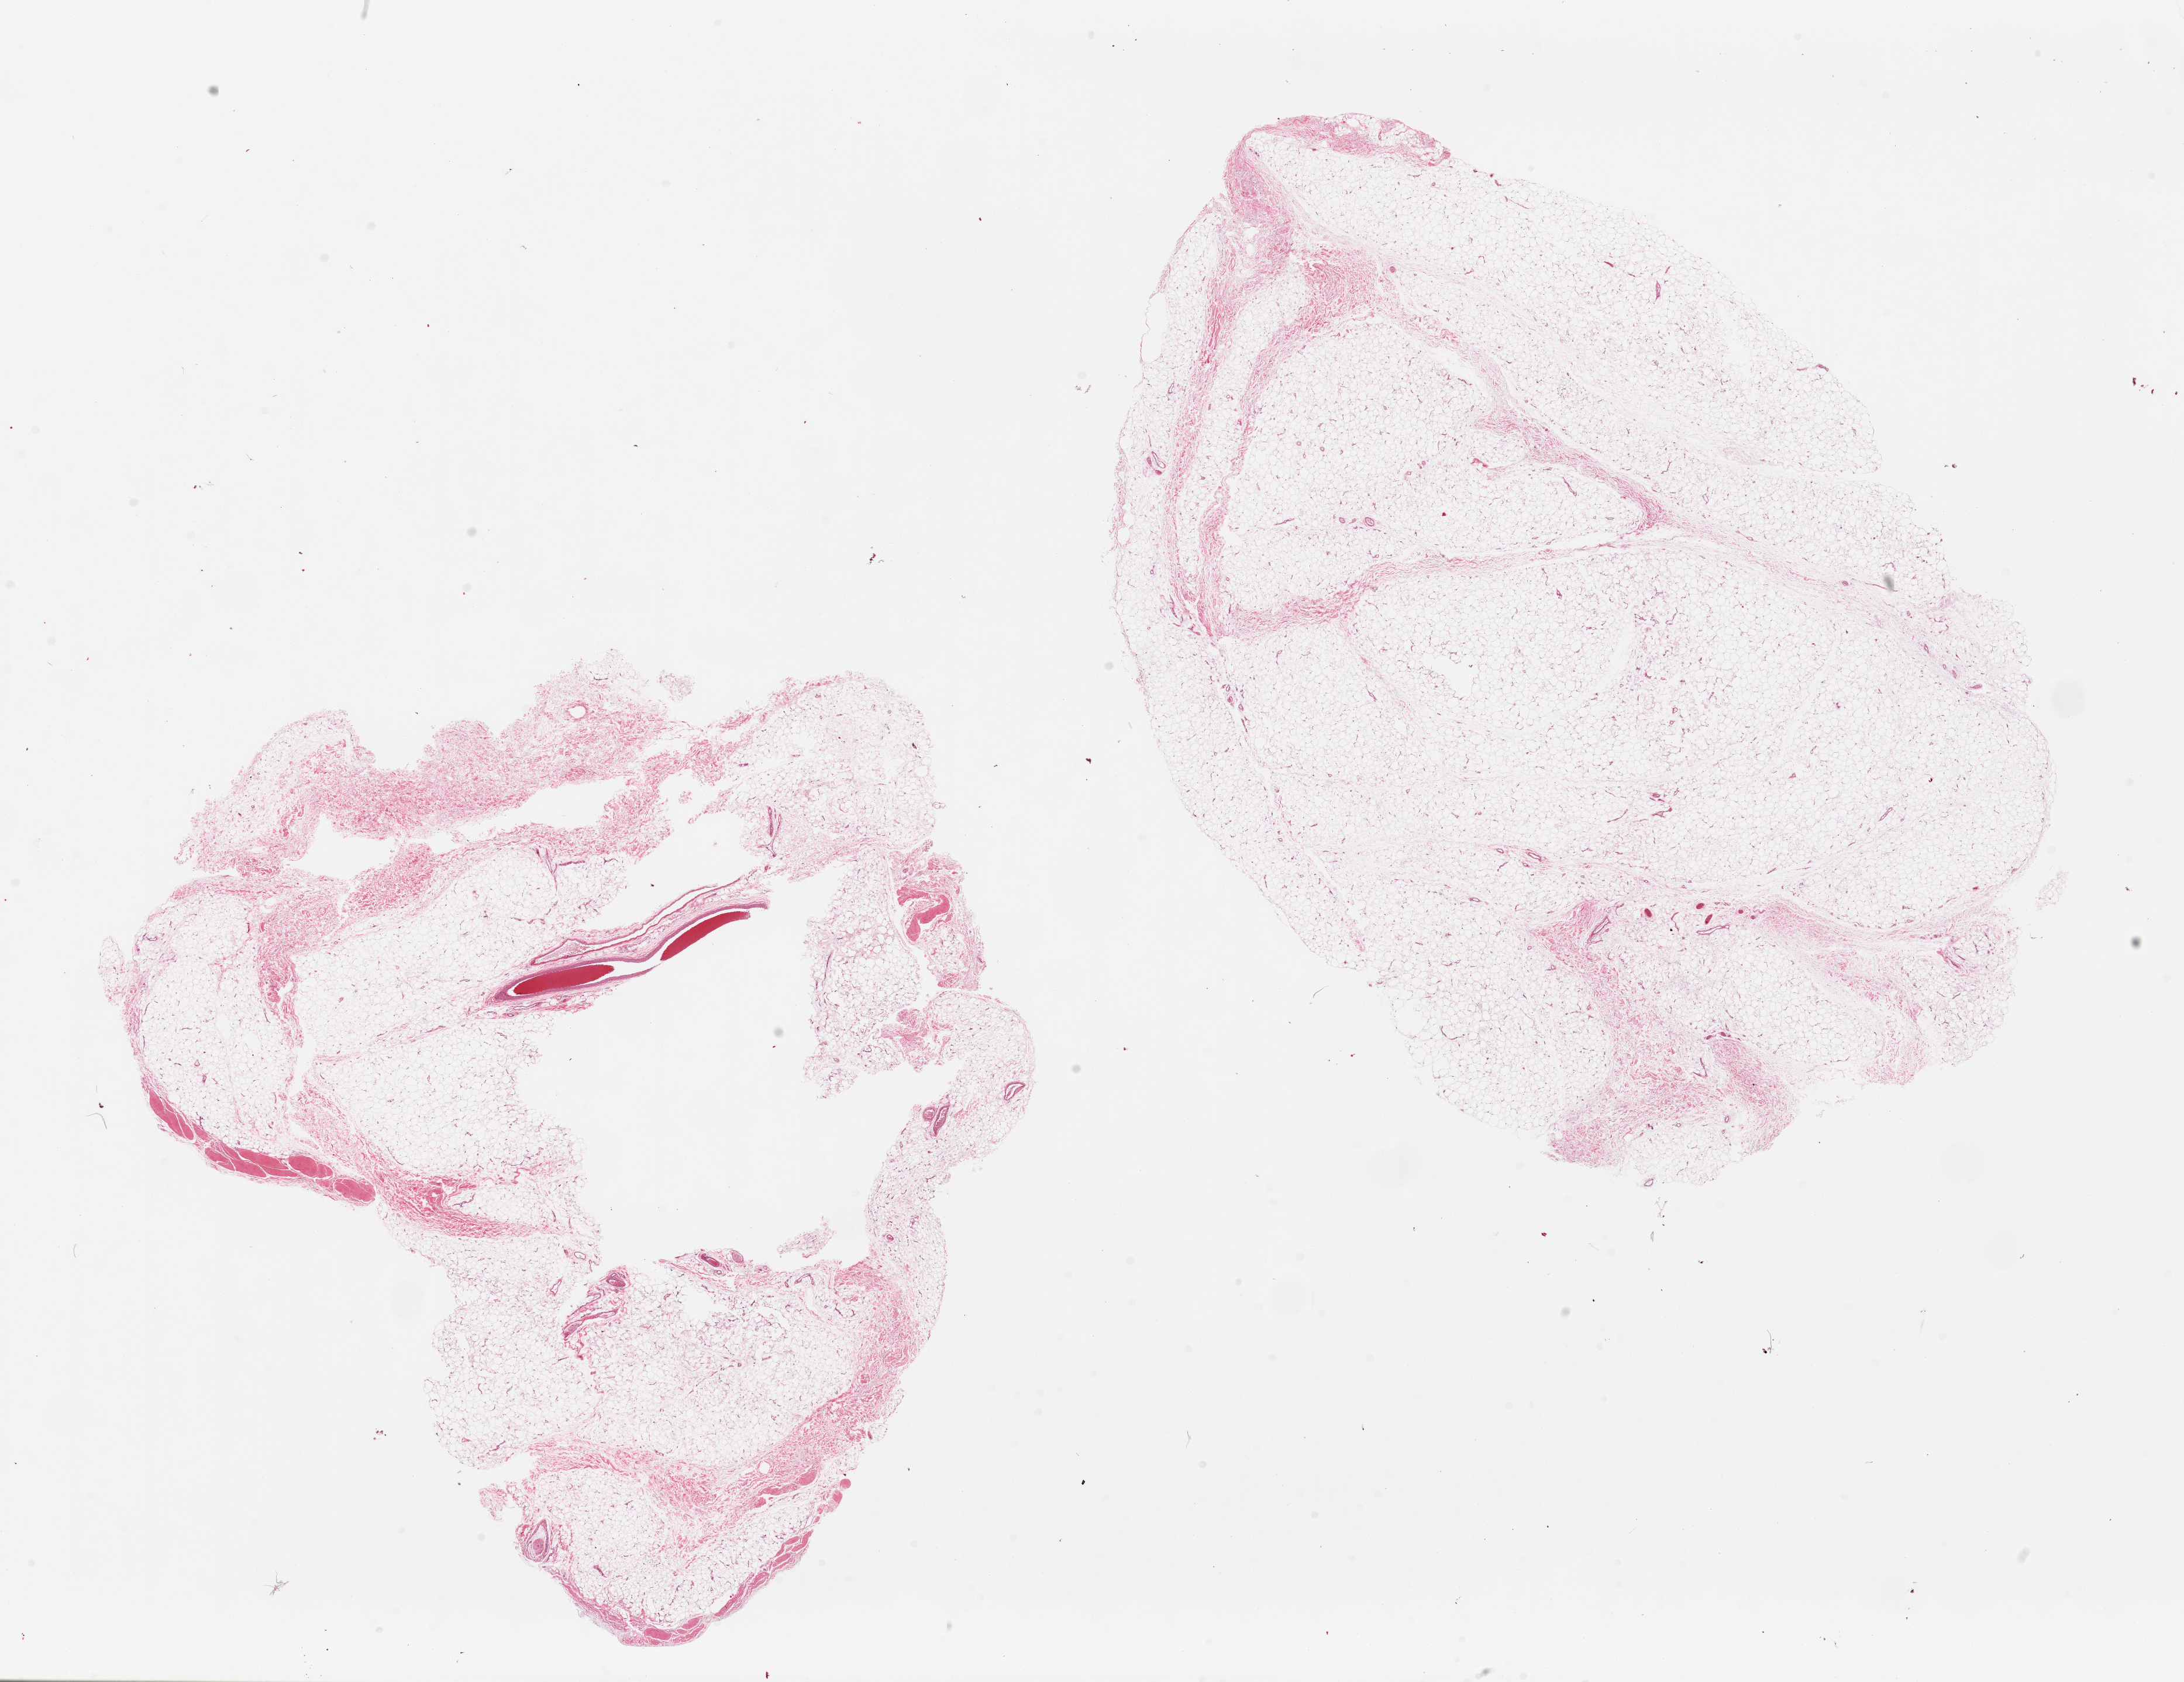
Haematoxylin and eosin whole-slide image, brightfield, whole scanned area (about 29.5 x 22.7 mm) shown as a low-resolution overview. PAXgene-fixed paraffin-embedded (PFPE) section. Section of adipose tissue (target tissue). Tissue donor sample. Male donor.
• review note (as recorded): 2 pieces; large central hole (unfixed)